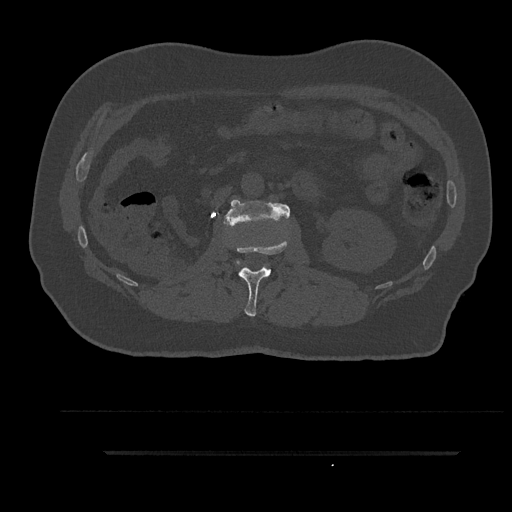
CT including the spine, one axial slice; slice 150 of 797 in the series (ordered by position); reconstruction kernel Br40s/3; 120 kVp; bone window (W 1800 / L 400 HU); 512 × 512 image matrix, field of view 432 × 432 mm. Patient: male, 63 years. Case-level facts recorded for this patient, not image findings: primary cancer: renal; vertebrae with lytic lesions (as recorded): T8.
Structures marked on this image (semi-automatically segmented with operator editing):
- L1 vertebra: box from (x=236, y=240) to (x=288, y=317) px
- L2 vertebra: (x=224, y=199)–(x=290, y=264)